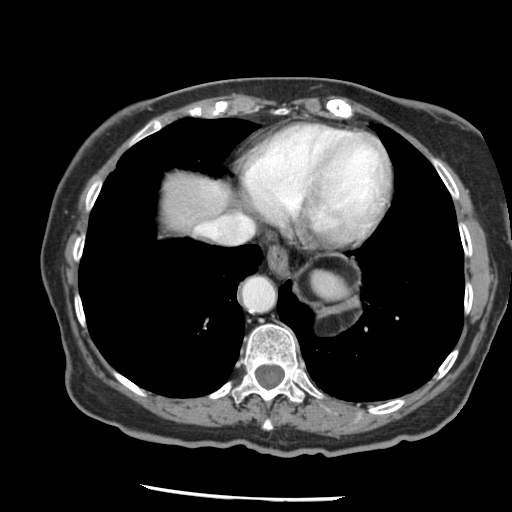
Contrast-enhanced abdominal CT, one axial slice; slice 120 of 148 in the series (ordered by position); reconstruction kernel STANDARD; intravenous contrast given; soft-tissue window (W 400 / L 40 HU); 2.5 mm slice thickness; 512 × 512 image matrix, field of view 330 × 330 mm. Female patient, age 85 years. From the clinical record (not read from this slice): diagnosis: colorectal cancer liver metastases, imaged before liver resection; multiple liver metastases: no; largest metastasis: 0.9 cm.
Structures marked on this image (outlined manually by an expert reader):
- hepatic veins: bounding box [x1, y1, x2, y2] px = [196, 215, 253, 244]
- liver: [158, 173, 231, 235]
- planned liver remnant (the part of the liver to remain after resection): [158, 173, 231, 235]